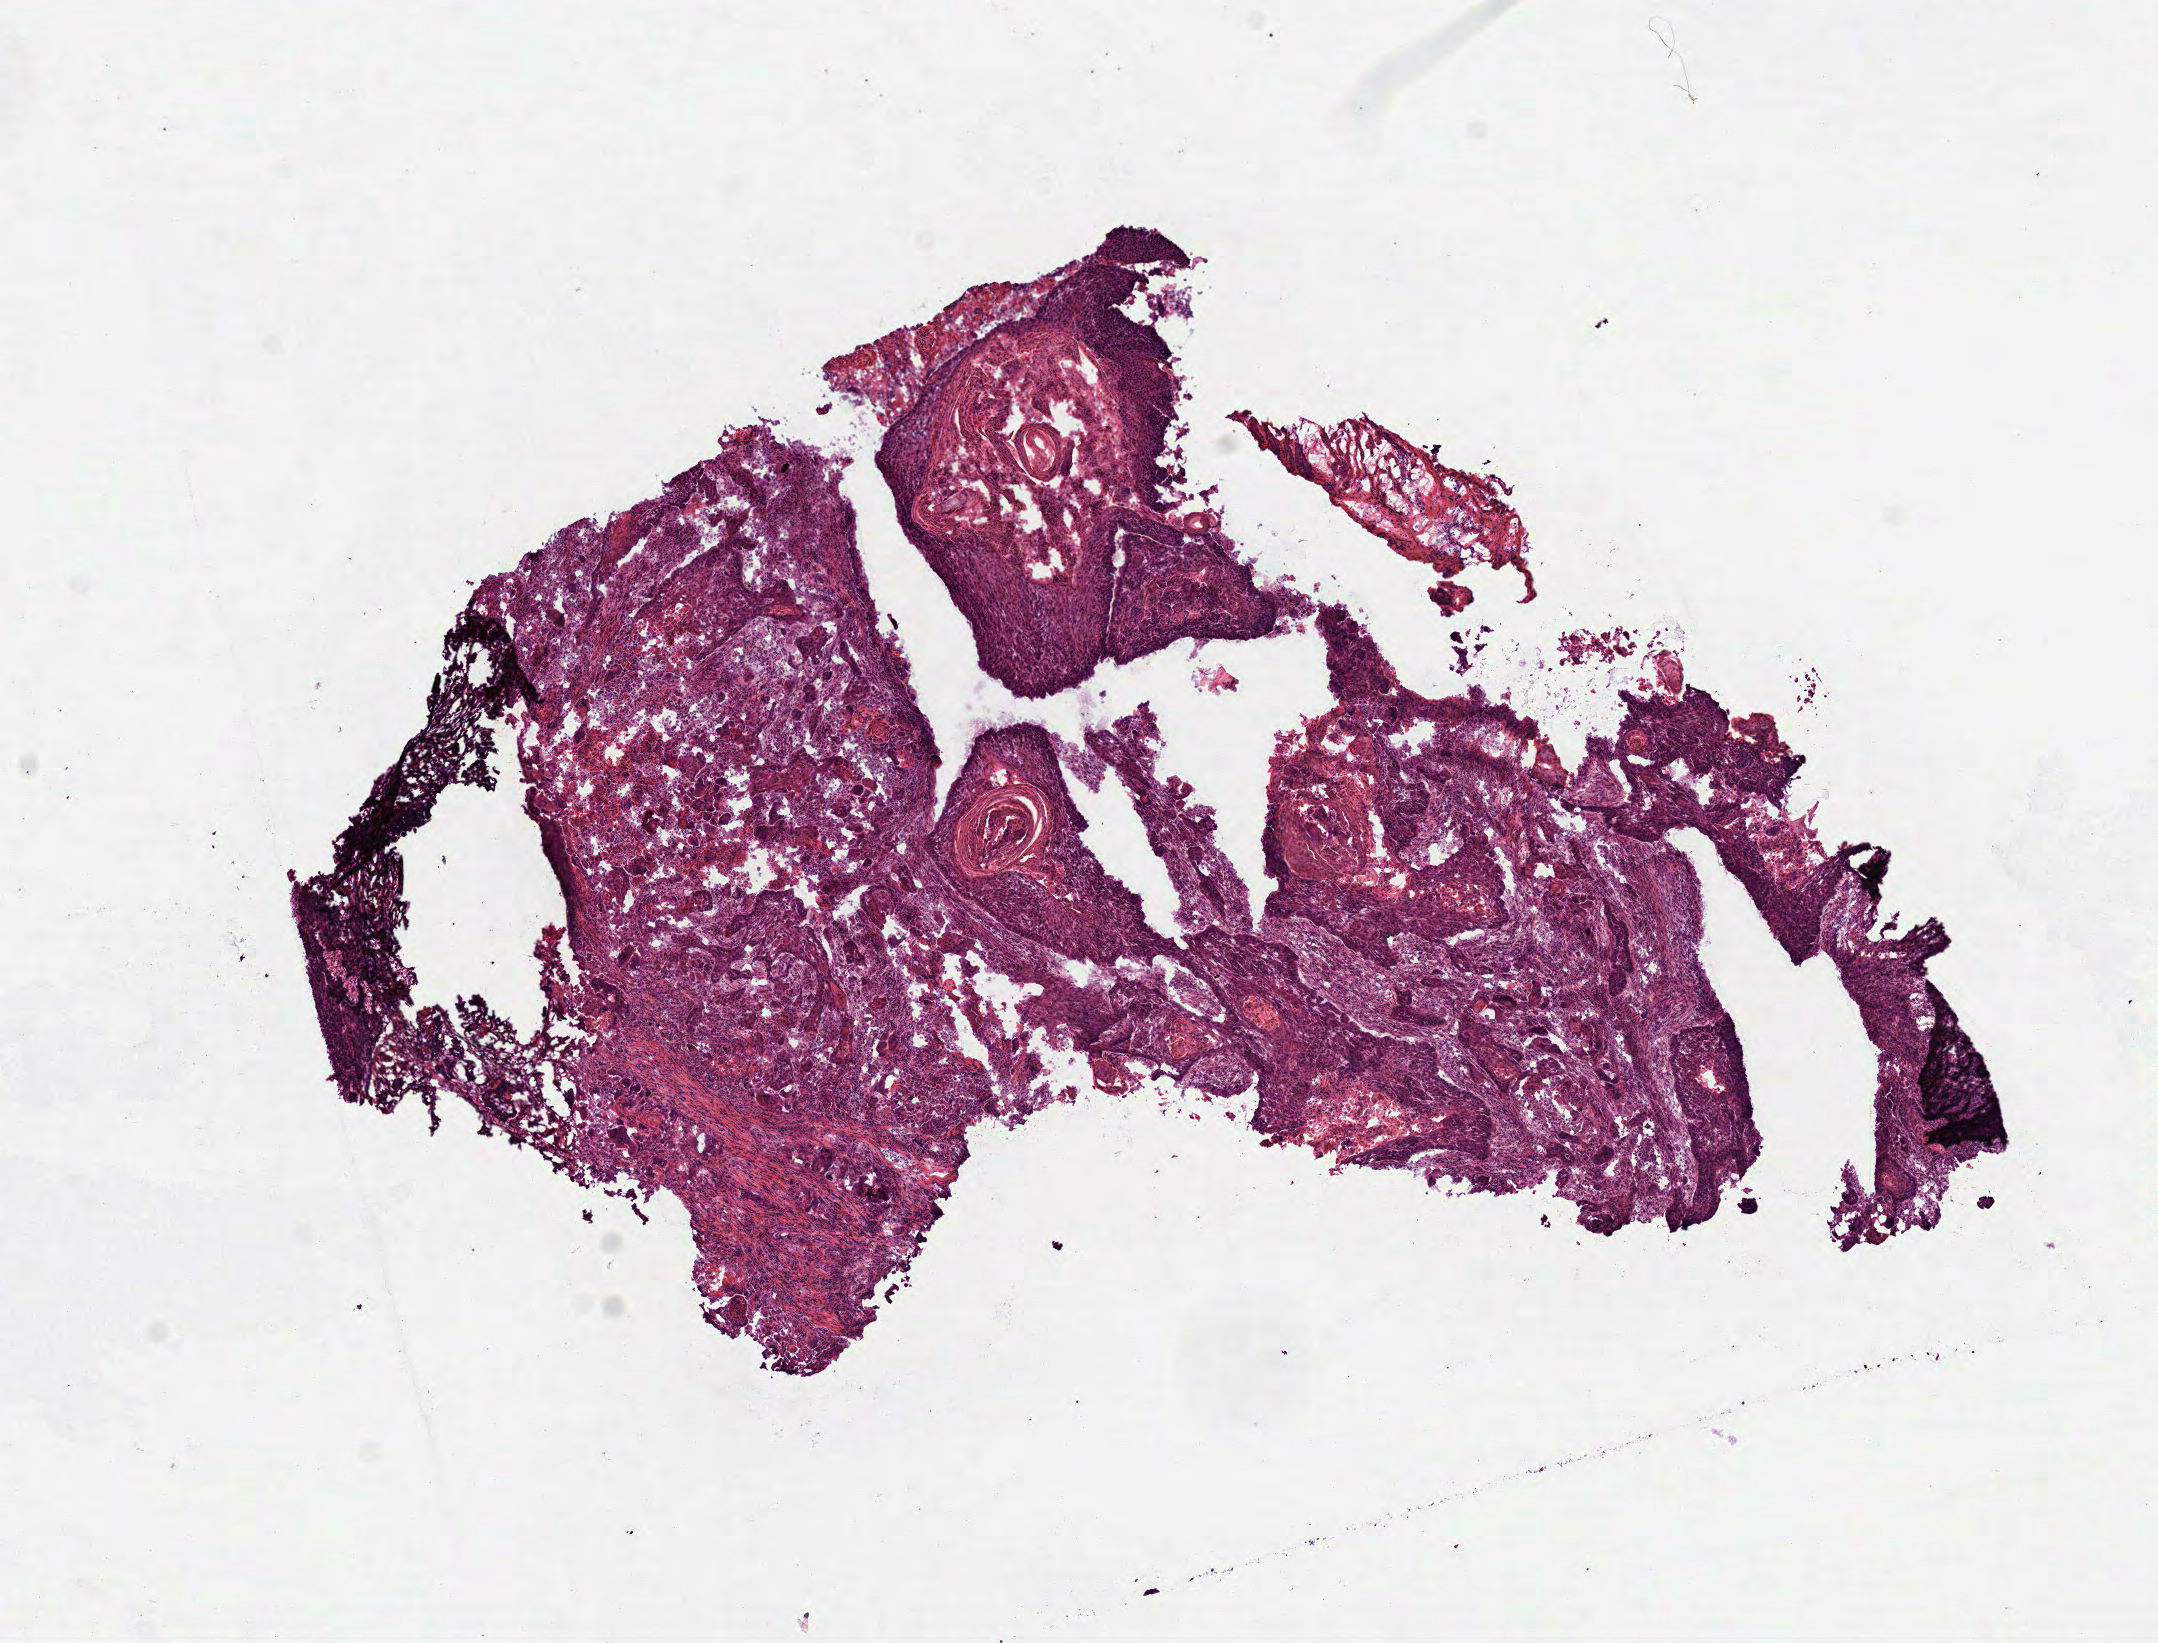
Whole-slide histology image, Hematoxylin and eosin (H&E) stained, low-resolution overview of the scanned area, about 8.7 x 6.6 mm (from a 40x scan); frozen section from the top of the tissue portion; primary tumour sample from the head and neck. Patient: male, age at initial diagnosis 53 years. Histologic grade: G2 (moderately differentiated). Composition of this section per pathologist review: tumour cells 100%, tumour nuclei 90%, normal cells 0%, stromal cells 0%, necrosis 0%. Inflammatory infiltration, as recorded: lymphocyte infiltration 2%, monocyte infiltration 0%, neutrophil infiltration 0%.
Lymph nodes positive (case pathology): 1 of 32 examined. AJCC pathologic stage: III (7th edition). Pathologic diagnosis: Squamous cell carcinoma, NOS (tongue, NOS).